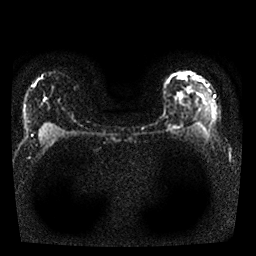
Breast MRI, one axial slice; diffusion-weighted series; image 2 of 4 stored at this slice position (different b-values; order by instance number); 1.5 T; 4 mm slice thickness; 256 × 256 image matrix, field of view 310 × 310 mm. Female patient.
Structures marked on this image (expert manual segmentation):
- tumour on diffusion-weighted imaging: bounding box <174,126,177,128> (left, top, right, bottom; pixels)